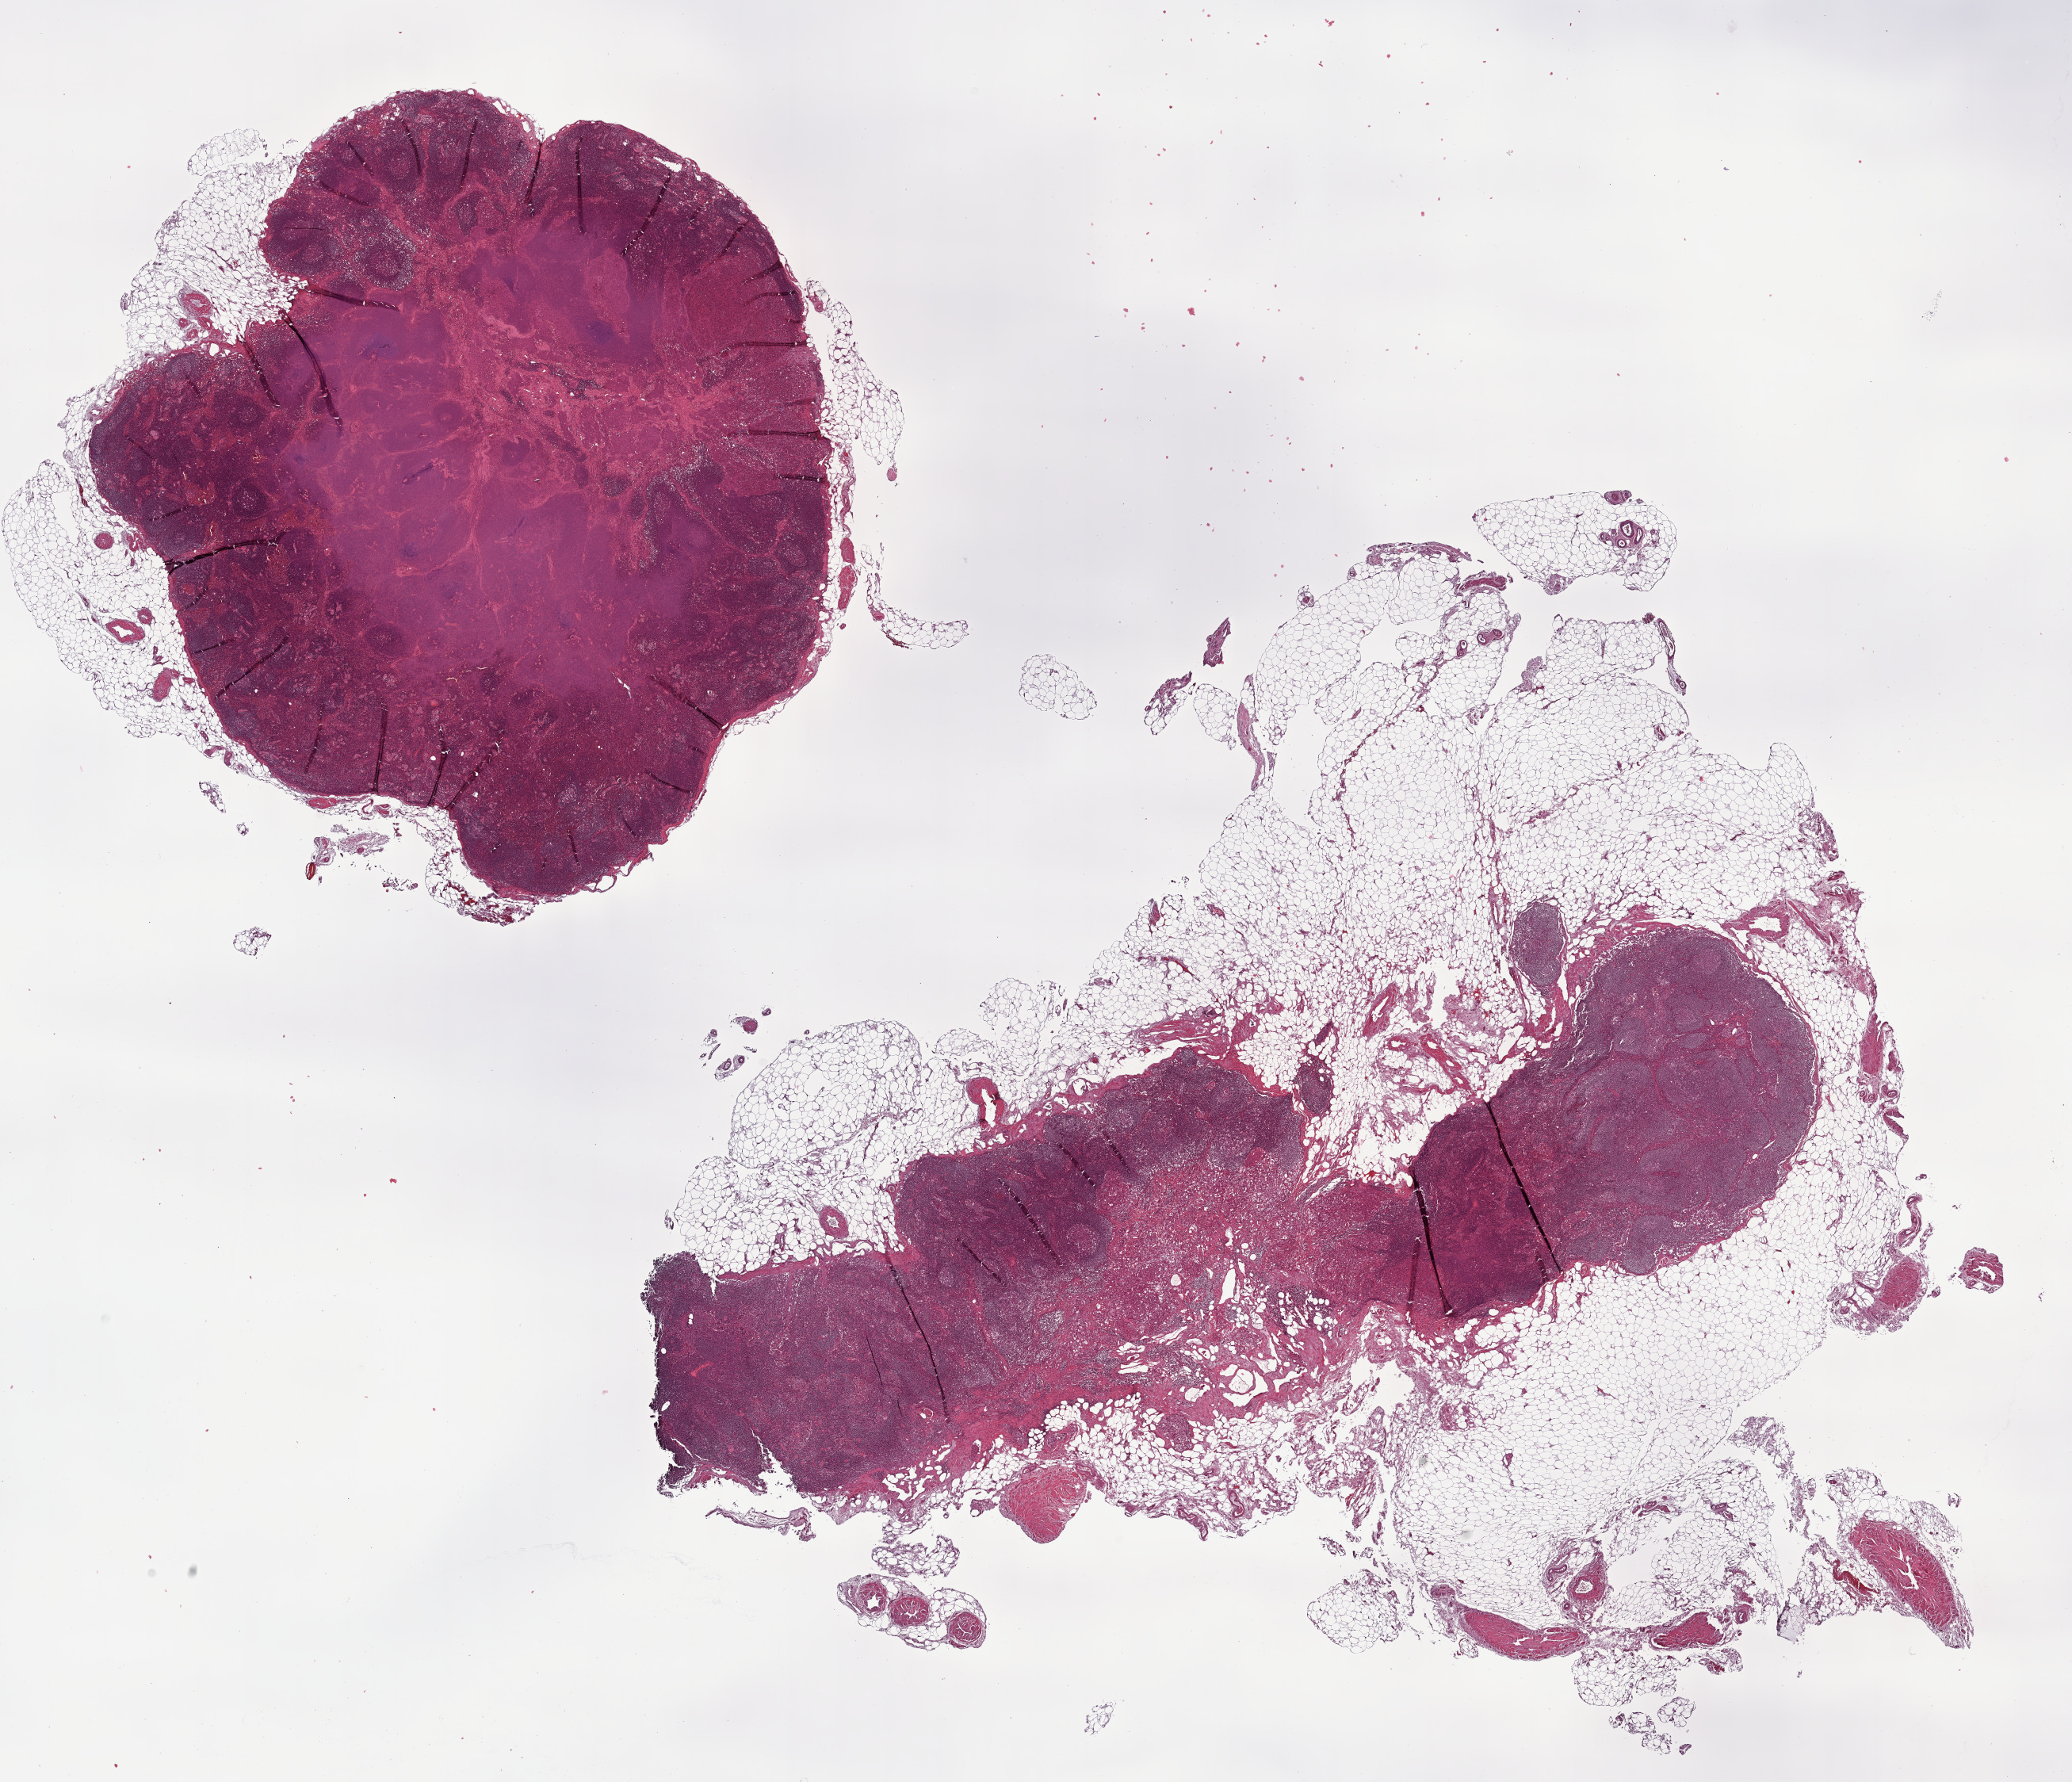
Whole-slide histology image, Hematoxylin and eosin (H&E) stained — shown as a low-resolution overview of the whole scanned area (about 21.1 x 18.2 mm, slide scanned at 40x). Formalin-fixed paraffin-embedded (FFPE) diagnostic section. Cervix, primary tumour sample. Patient: female, age at initial diagnosis 79 years. Histologic grade: G2 (moderately differentiated).
Diagnosis: Squamous cell carcinoma, NOS (cervix uteri). Lymph nodes positive (case pathology): 3 of 23 examined. FIGO stage: IB1.